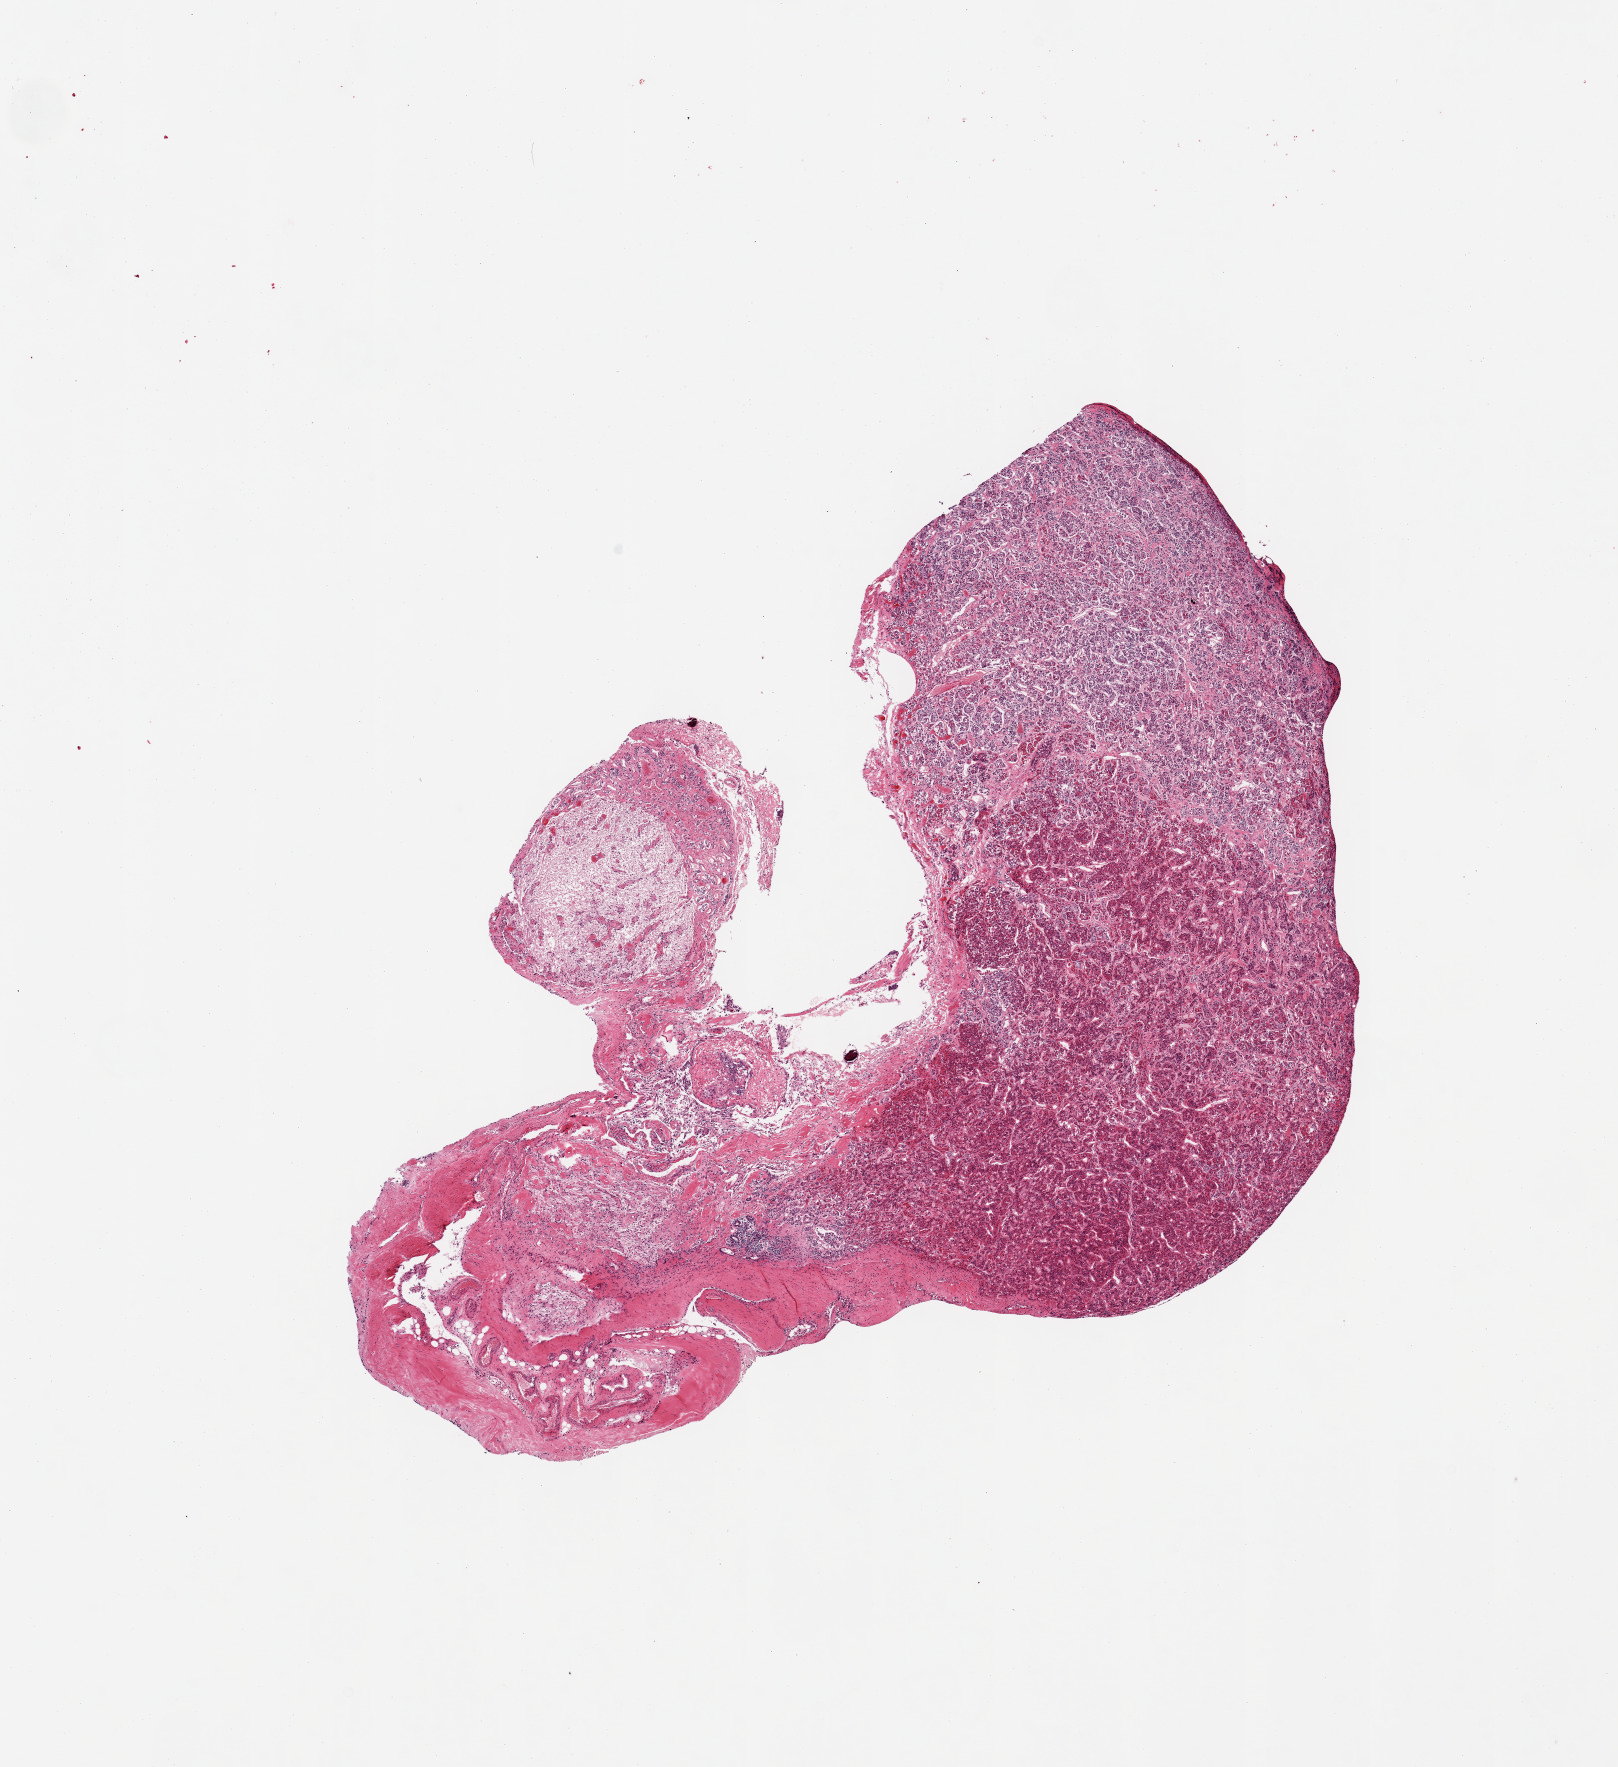
Whole-slide image, hematoxylin and eosin (H&E) stain — low-resolution overview of the scanned area, about 12.8 x 14.0 mm (acquisition: 20x scan); PAXgene-fixed, paraffin-embedded tissue; sampled site (target tissue): pituitary; donor tissue sample. Donor: male.
Pathologist's review note for this sample: 1 piece; 50% anterior, 25% posterior, 25% fibrous tissue.